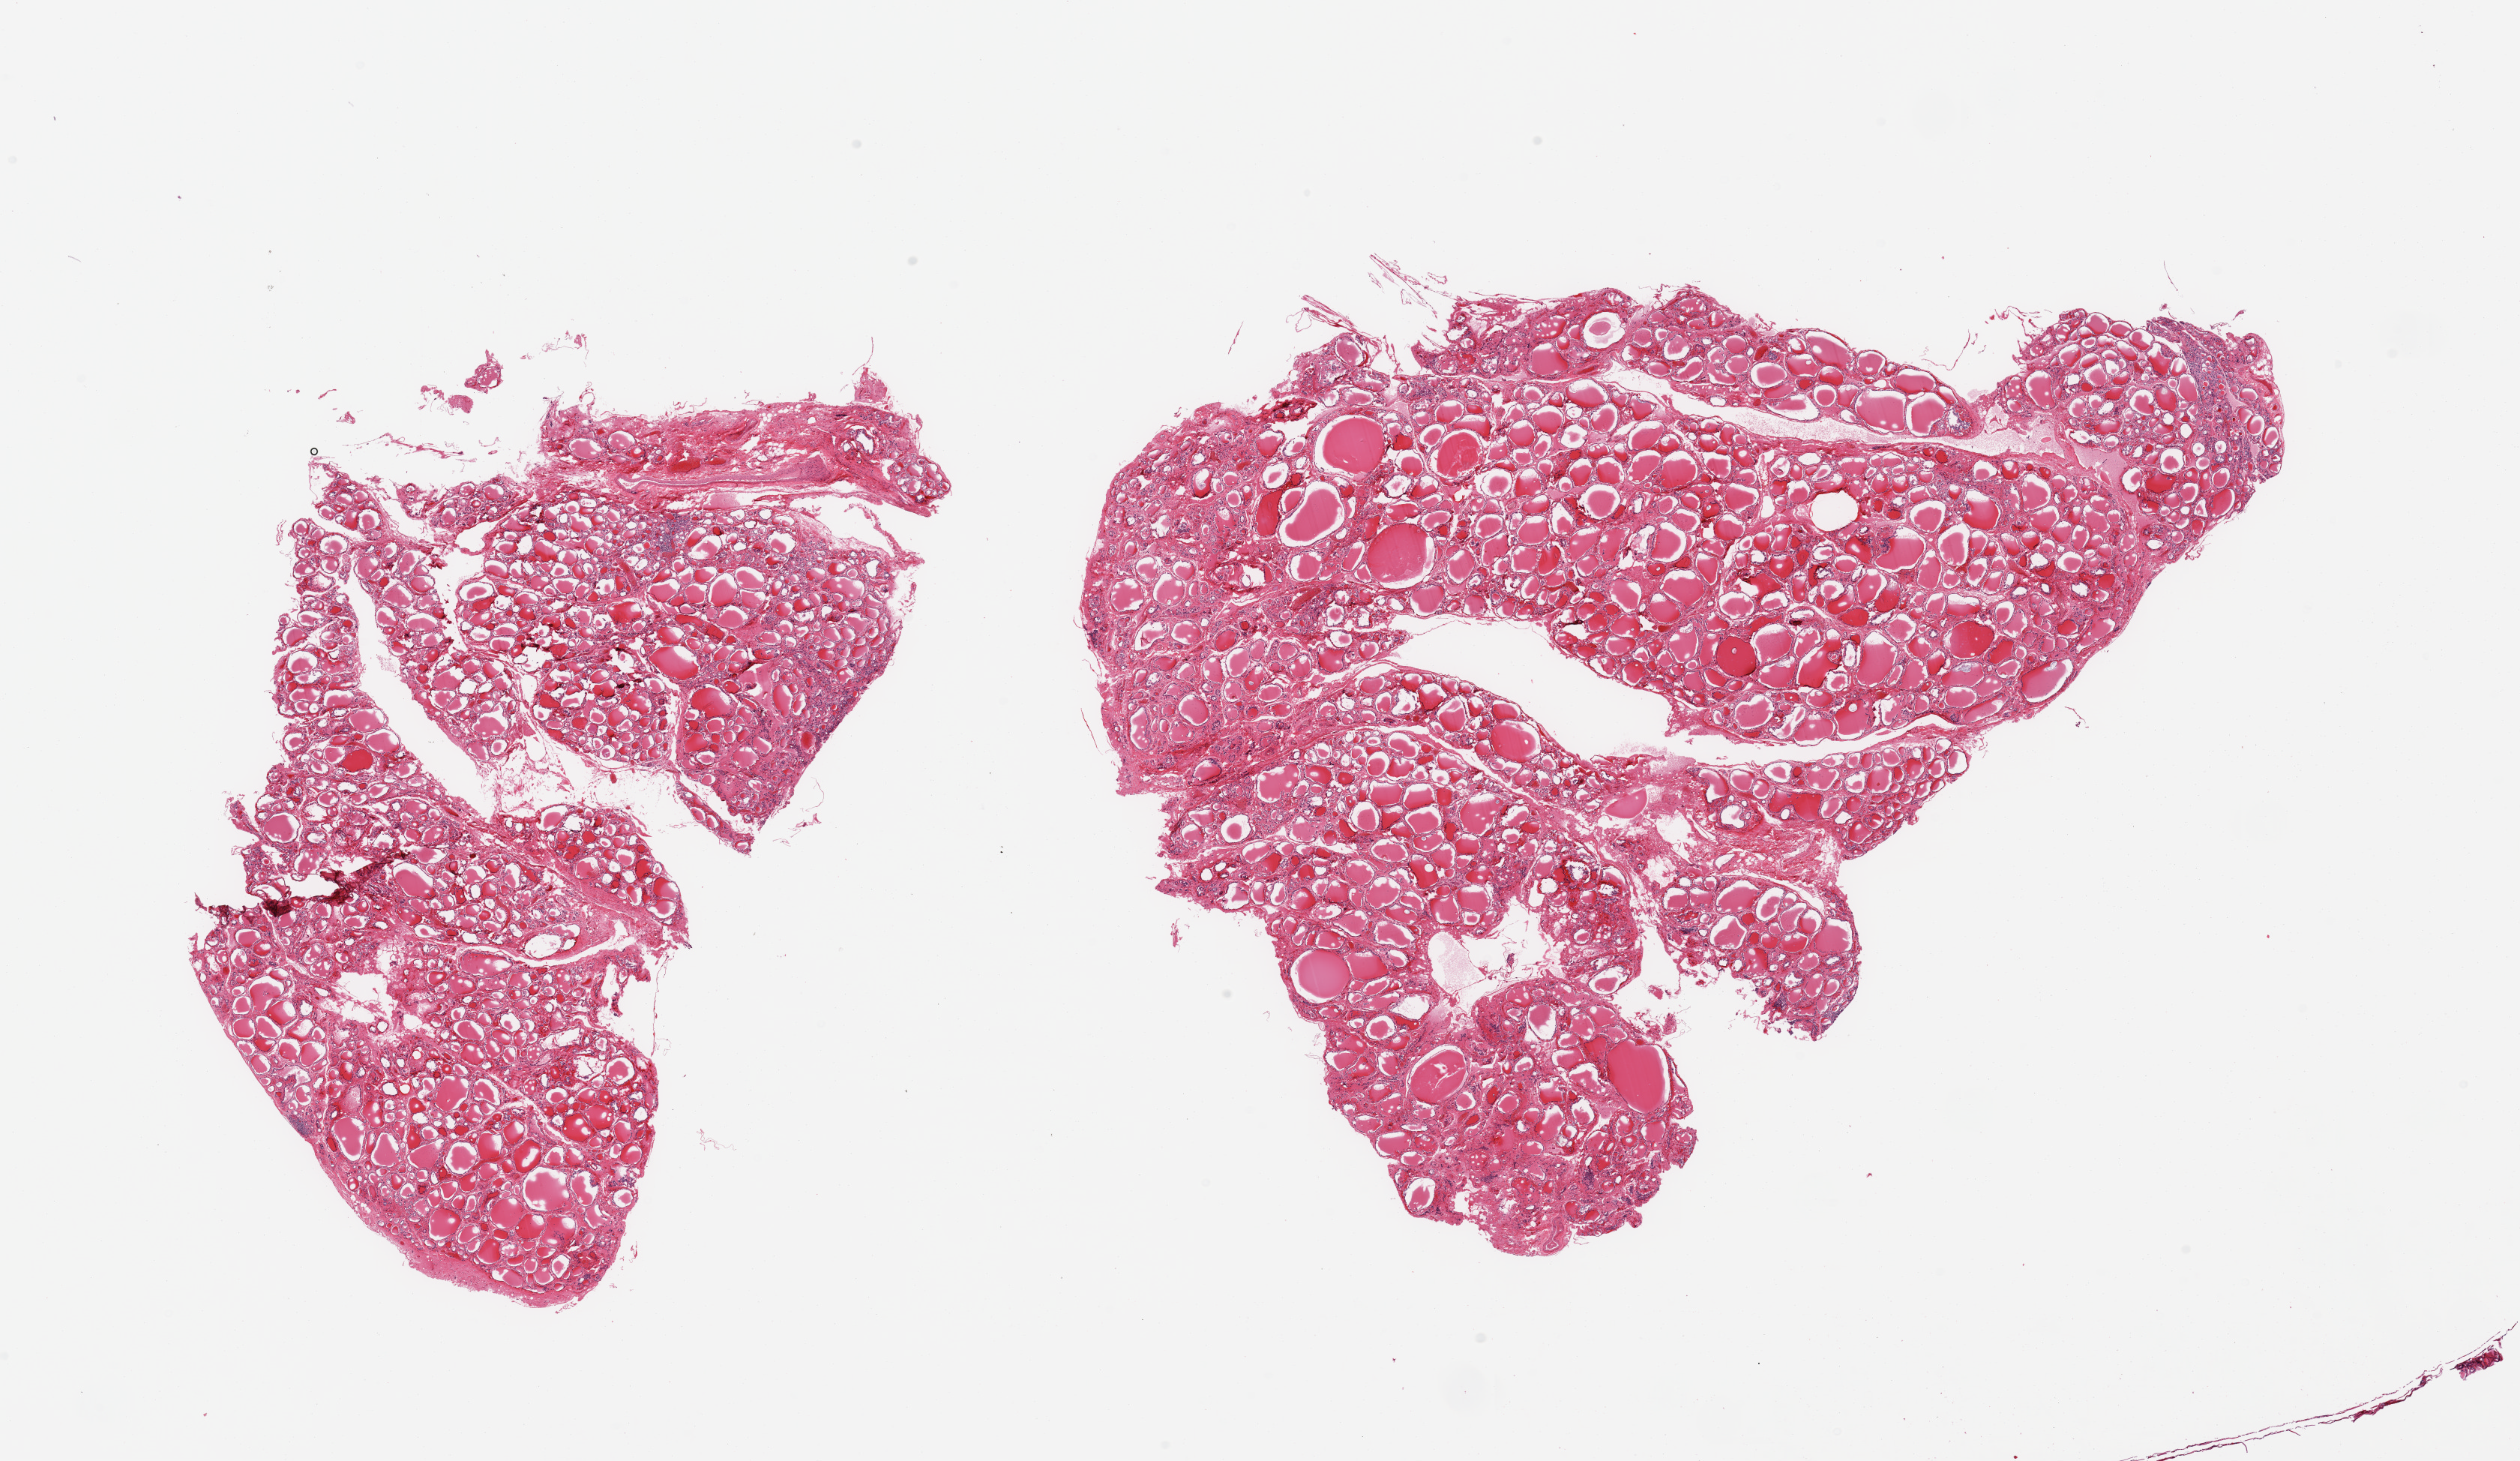
H&E whole-slide image, brightfield — whole scanned area (about 26.6 x 15.4 mm, from a 20x scan) shown as a low-resolution overview, PAXgene-fixed, paraffin-embedded tissue, target tissue: thyroid, tissue donor sample. Donor sex: male.
Review note (as recorded): 2 pieces; minute 0.3mm lymphoid or parathyroid focus.